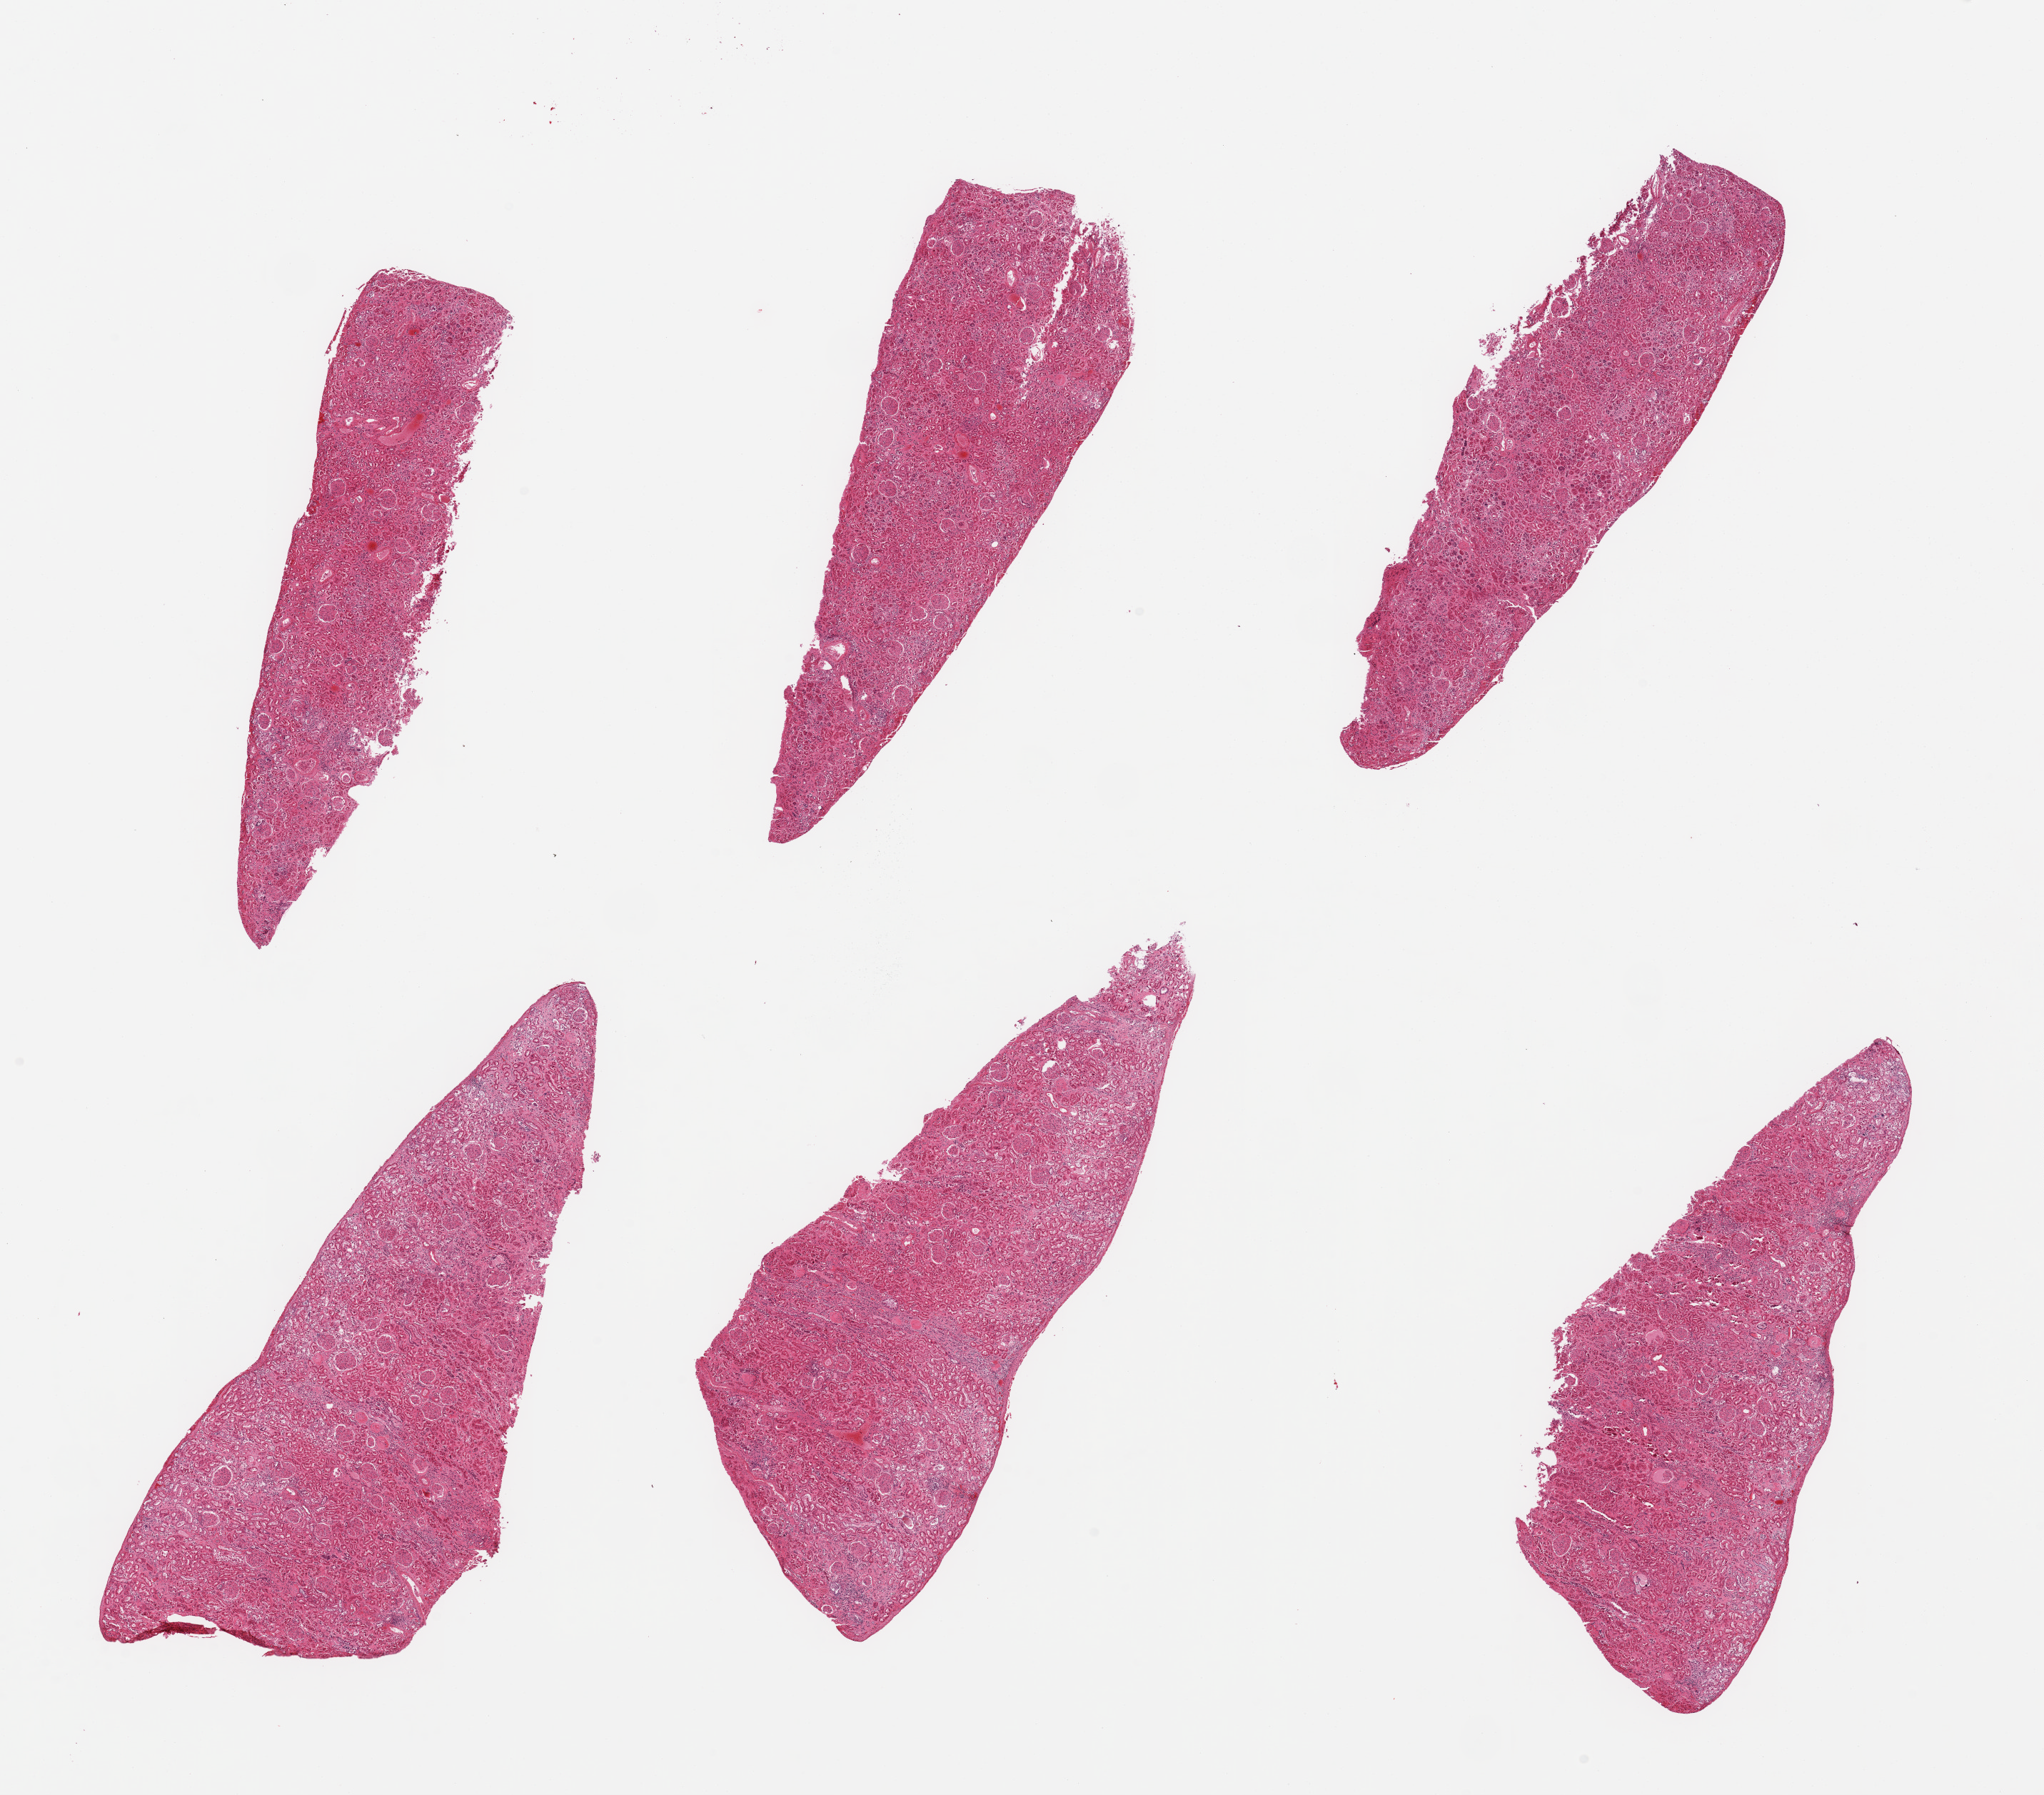
H&E whole-slide image — low-resolution overview of the scanned area, about 22.6 x 19.9 mm (slide scanned at 20x), PAXgene-fixed, paraffin-embedded tissue, target tissue: renal cortex, donor tissue sample. Male donor.
Review note (as recorded): 6 pieces; several small old inflammatory lesions.